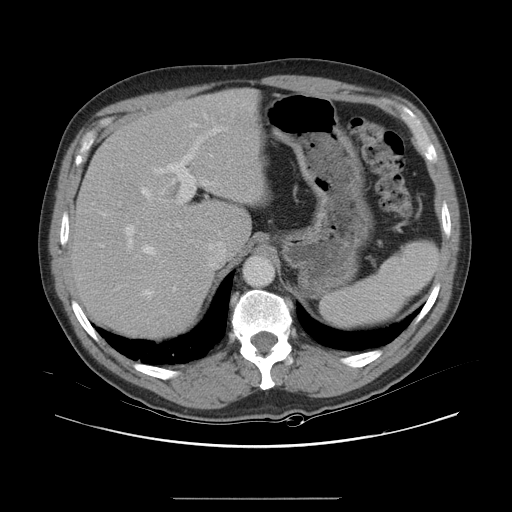
Contrast-enhanced abdominal CT, one axial slice. Slice 20 of 40 in the series (ordered by position). Intravenous contrast given. Soft-tissue window (W 400 / L 40 HU). 512 × 512 image matrix, field of view 408 × 408 mm. Male patient, age 64 years. Case-level facts recorded for this patient, not image findings: diagnosis: colorectal cancer liver metastases, imaged before liver resection; multiple liver metastases: yes; largest metastasis: 3.2 cm; disease in both lobes: yes.
Outlined on this slice (outlined manually by an expert reader):
- hepatic veins: bounding box (x1, y1, x2, y2) in pixels: (101, 188, 155, 298)
- liver: (75, 91, 260, 336)
- planned liver remnant (the part of the liver to remain after resection): (87, 91, 260, 250)
- portal vein (with intrahepatic branches): (125, 125, 219, 292)